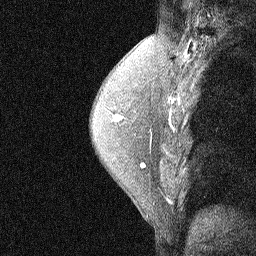
Breast MRI (dynamic contrast-enhanced), one sagittal slice. Position 39 of 58 along the scan axis. Dynamic contrast-enhanced study with each time point stored as its own series, time point 2 of 3 at this slice position (early post-contrast, ordered by acquisition time). 1.5 T. TE 4.5 ms, TR 11 ms. 2.07 mm slice thickness. 256 × 256 image matrix, field of view 200 × 200 mm. Patient: female, 54 years. Case-level facts recorded for this patient, not image findings: setting: breast cancer imaged before/during neoadjuvant chemotherapy; receptor status: HR-positive, HER2-negative.
Annotated regions visible in this slice (semi-automatic segmentation, software-assisted and operator-edited):
- analysis volume of interest (the breast-tissue region the enhancement analysis was run in; not a lesion): box from (x=92, y=89) to (x=149, y=186) px
- tumour enhancement mask (voxels above the 90 % enhancement threshold inside the analysis volume of interest): (x=117, y=116)–(x=123, y=120)